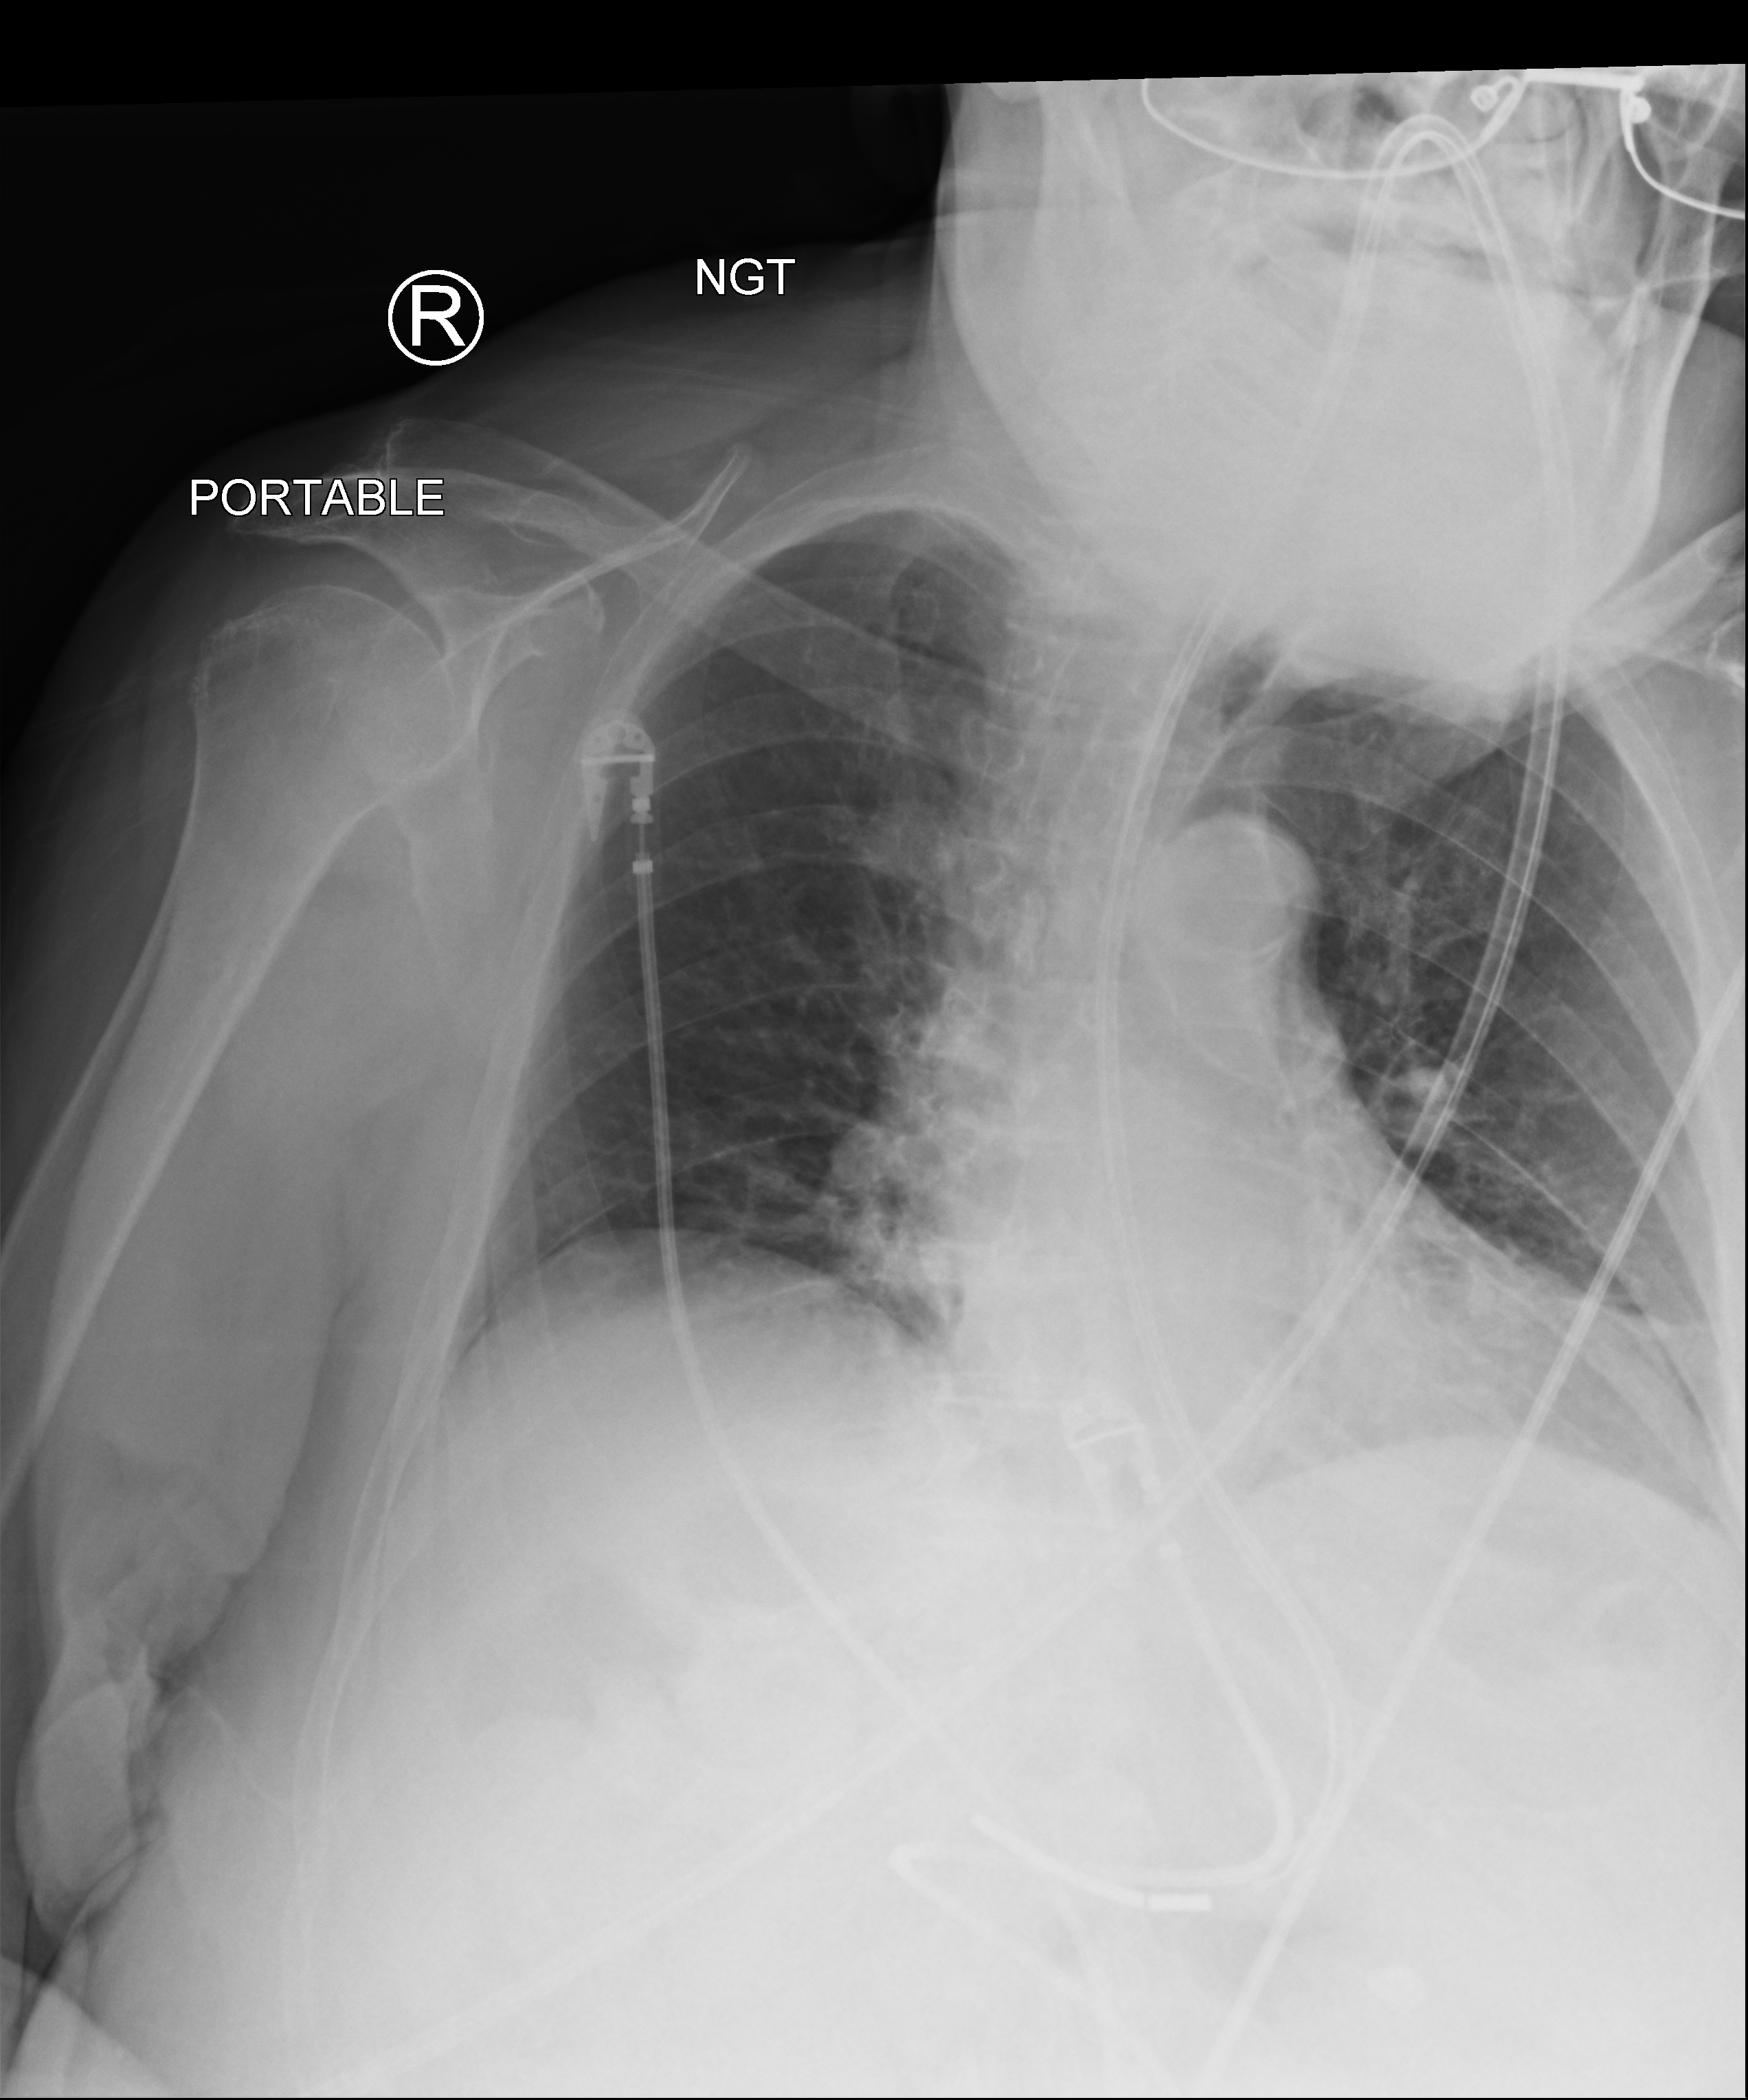
Portable chest radiograph; anteroposterior (AP) projection. Patient hospitalised with COVID-19; female, aged 75–90 years.
Hospital-stay facts (about this admission, not read from this image; timing relative to this image not recorded):
- mechanically ventilated during this hospital stay: no
- admitted to intensive care during this hospital stay: no